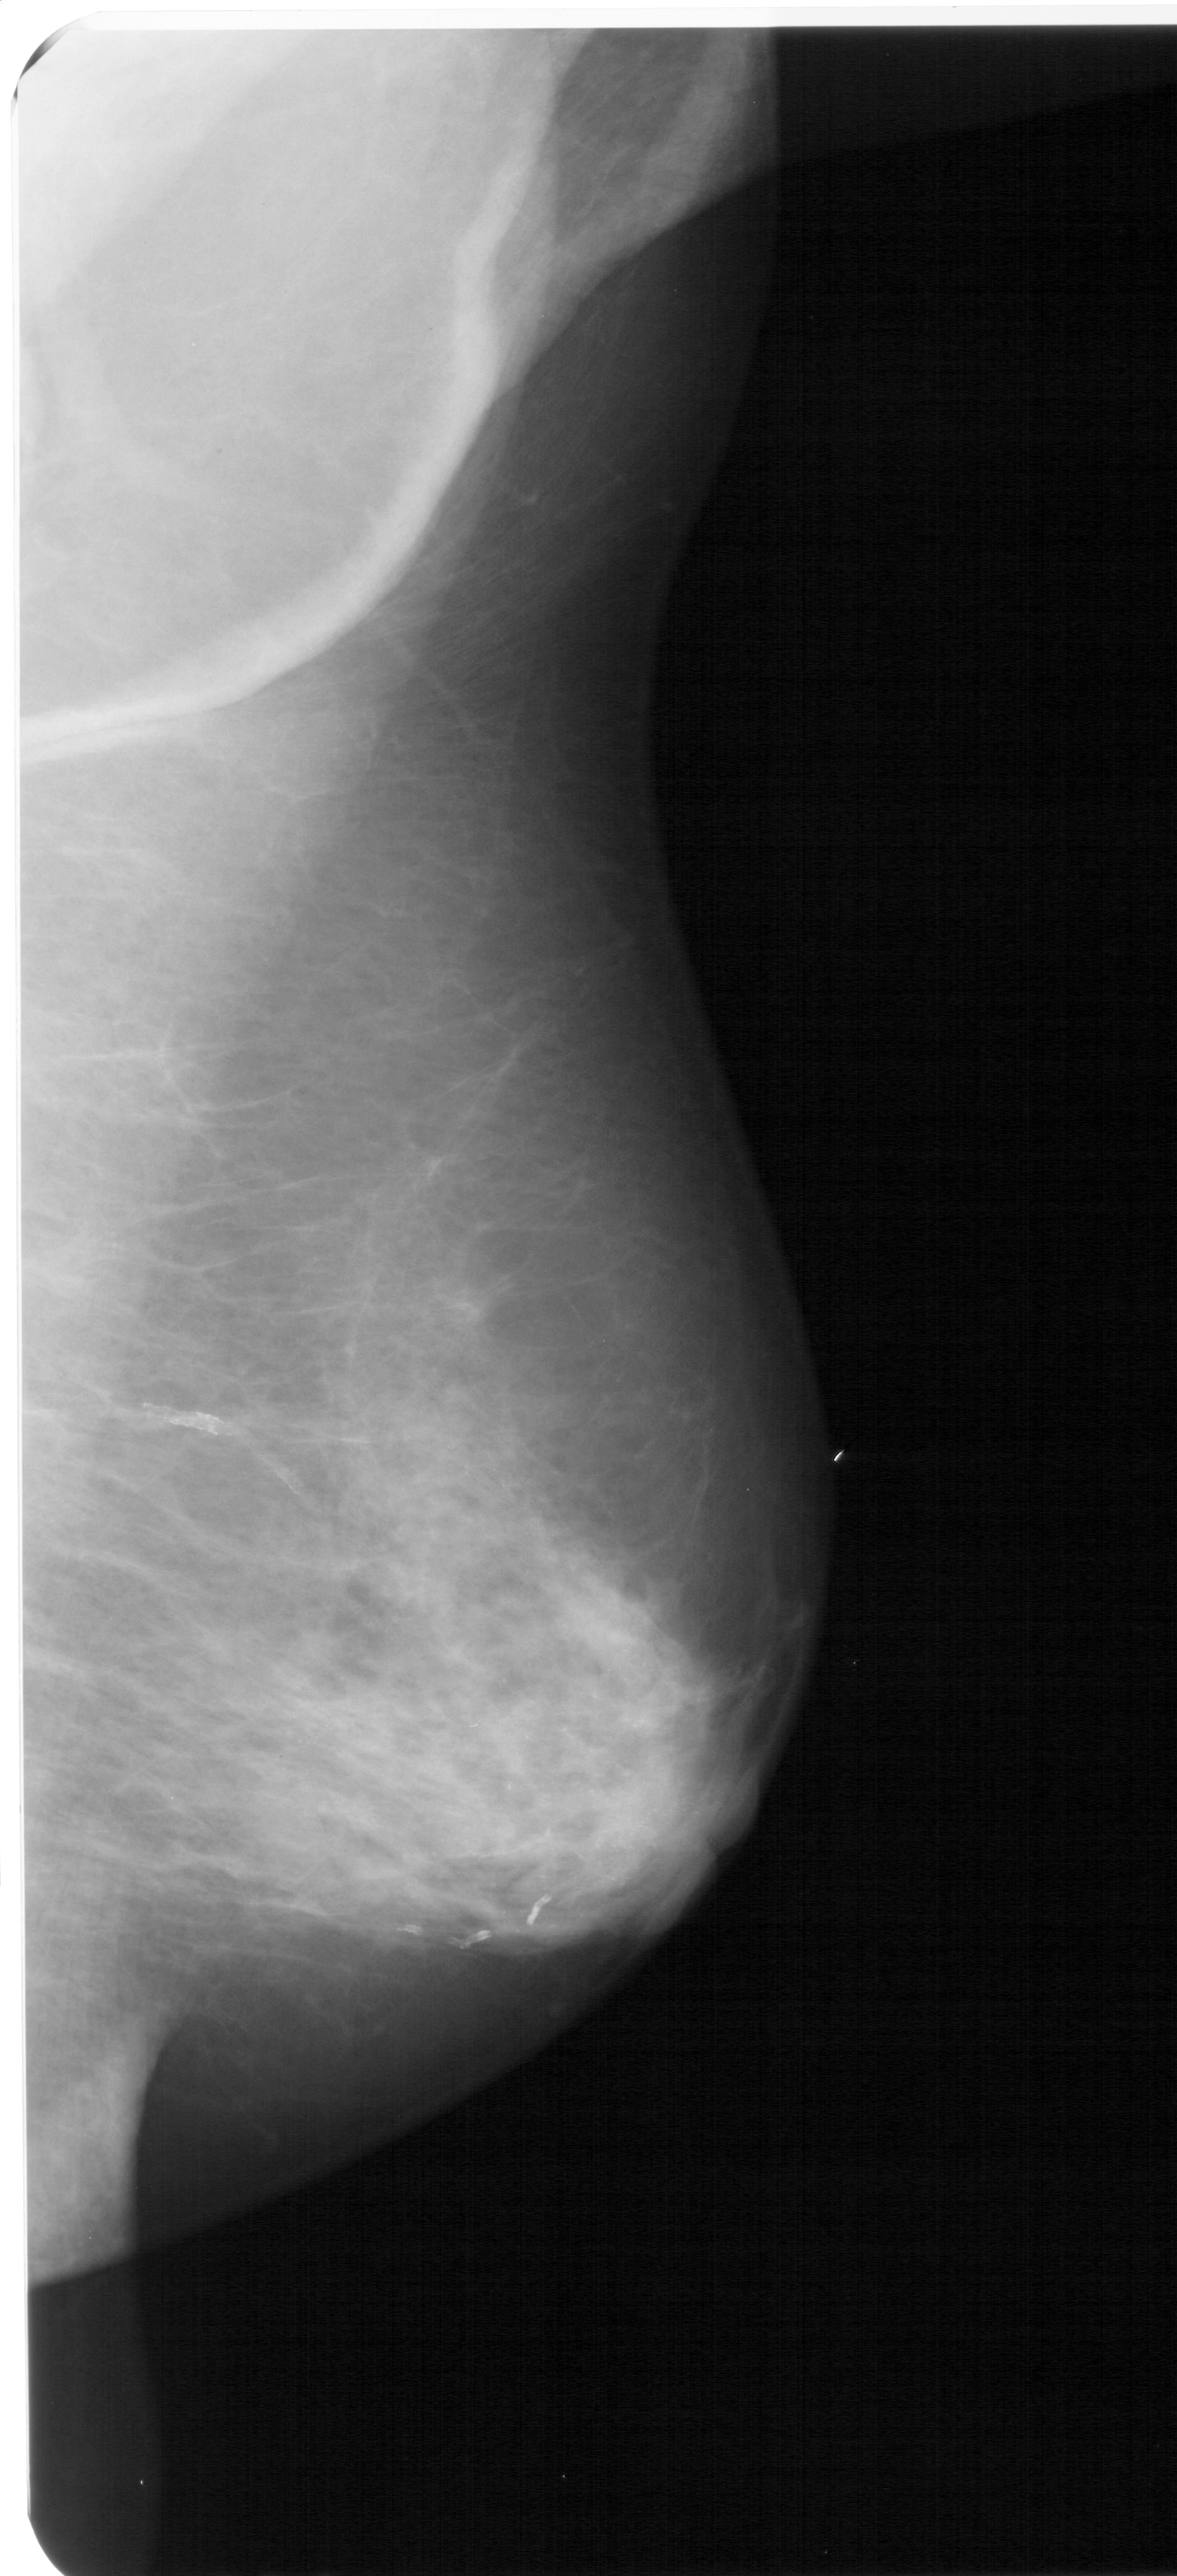
Scanned film-screen mammogram; right breast; mediolateral oblique (MLO) view; breast composition: extremely dense (BI-RADS density category 4 of 4); 1177 × 2576 image matrix.
Expert-marked regions of interest on this film, with their recorded descriptors:
- calcifications, morphology punctate / amorphous, distribution regional; BI-RADS assessment category 4; pathology (as recorded): benign: bounding box (x1, y1, x2, y2) in pixels: (330, 1524, 760, 2000)